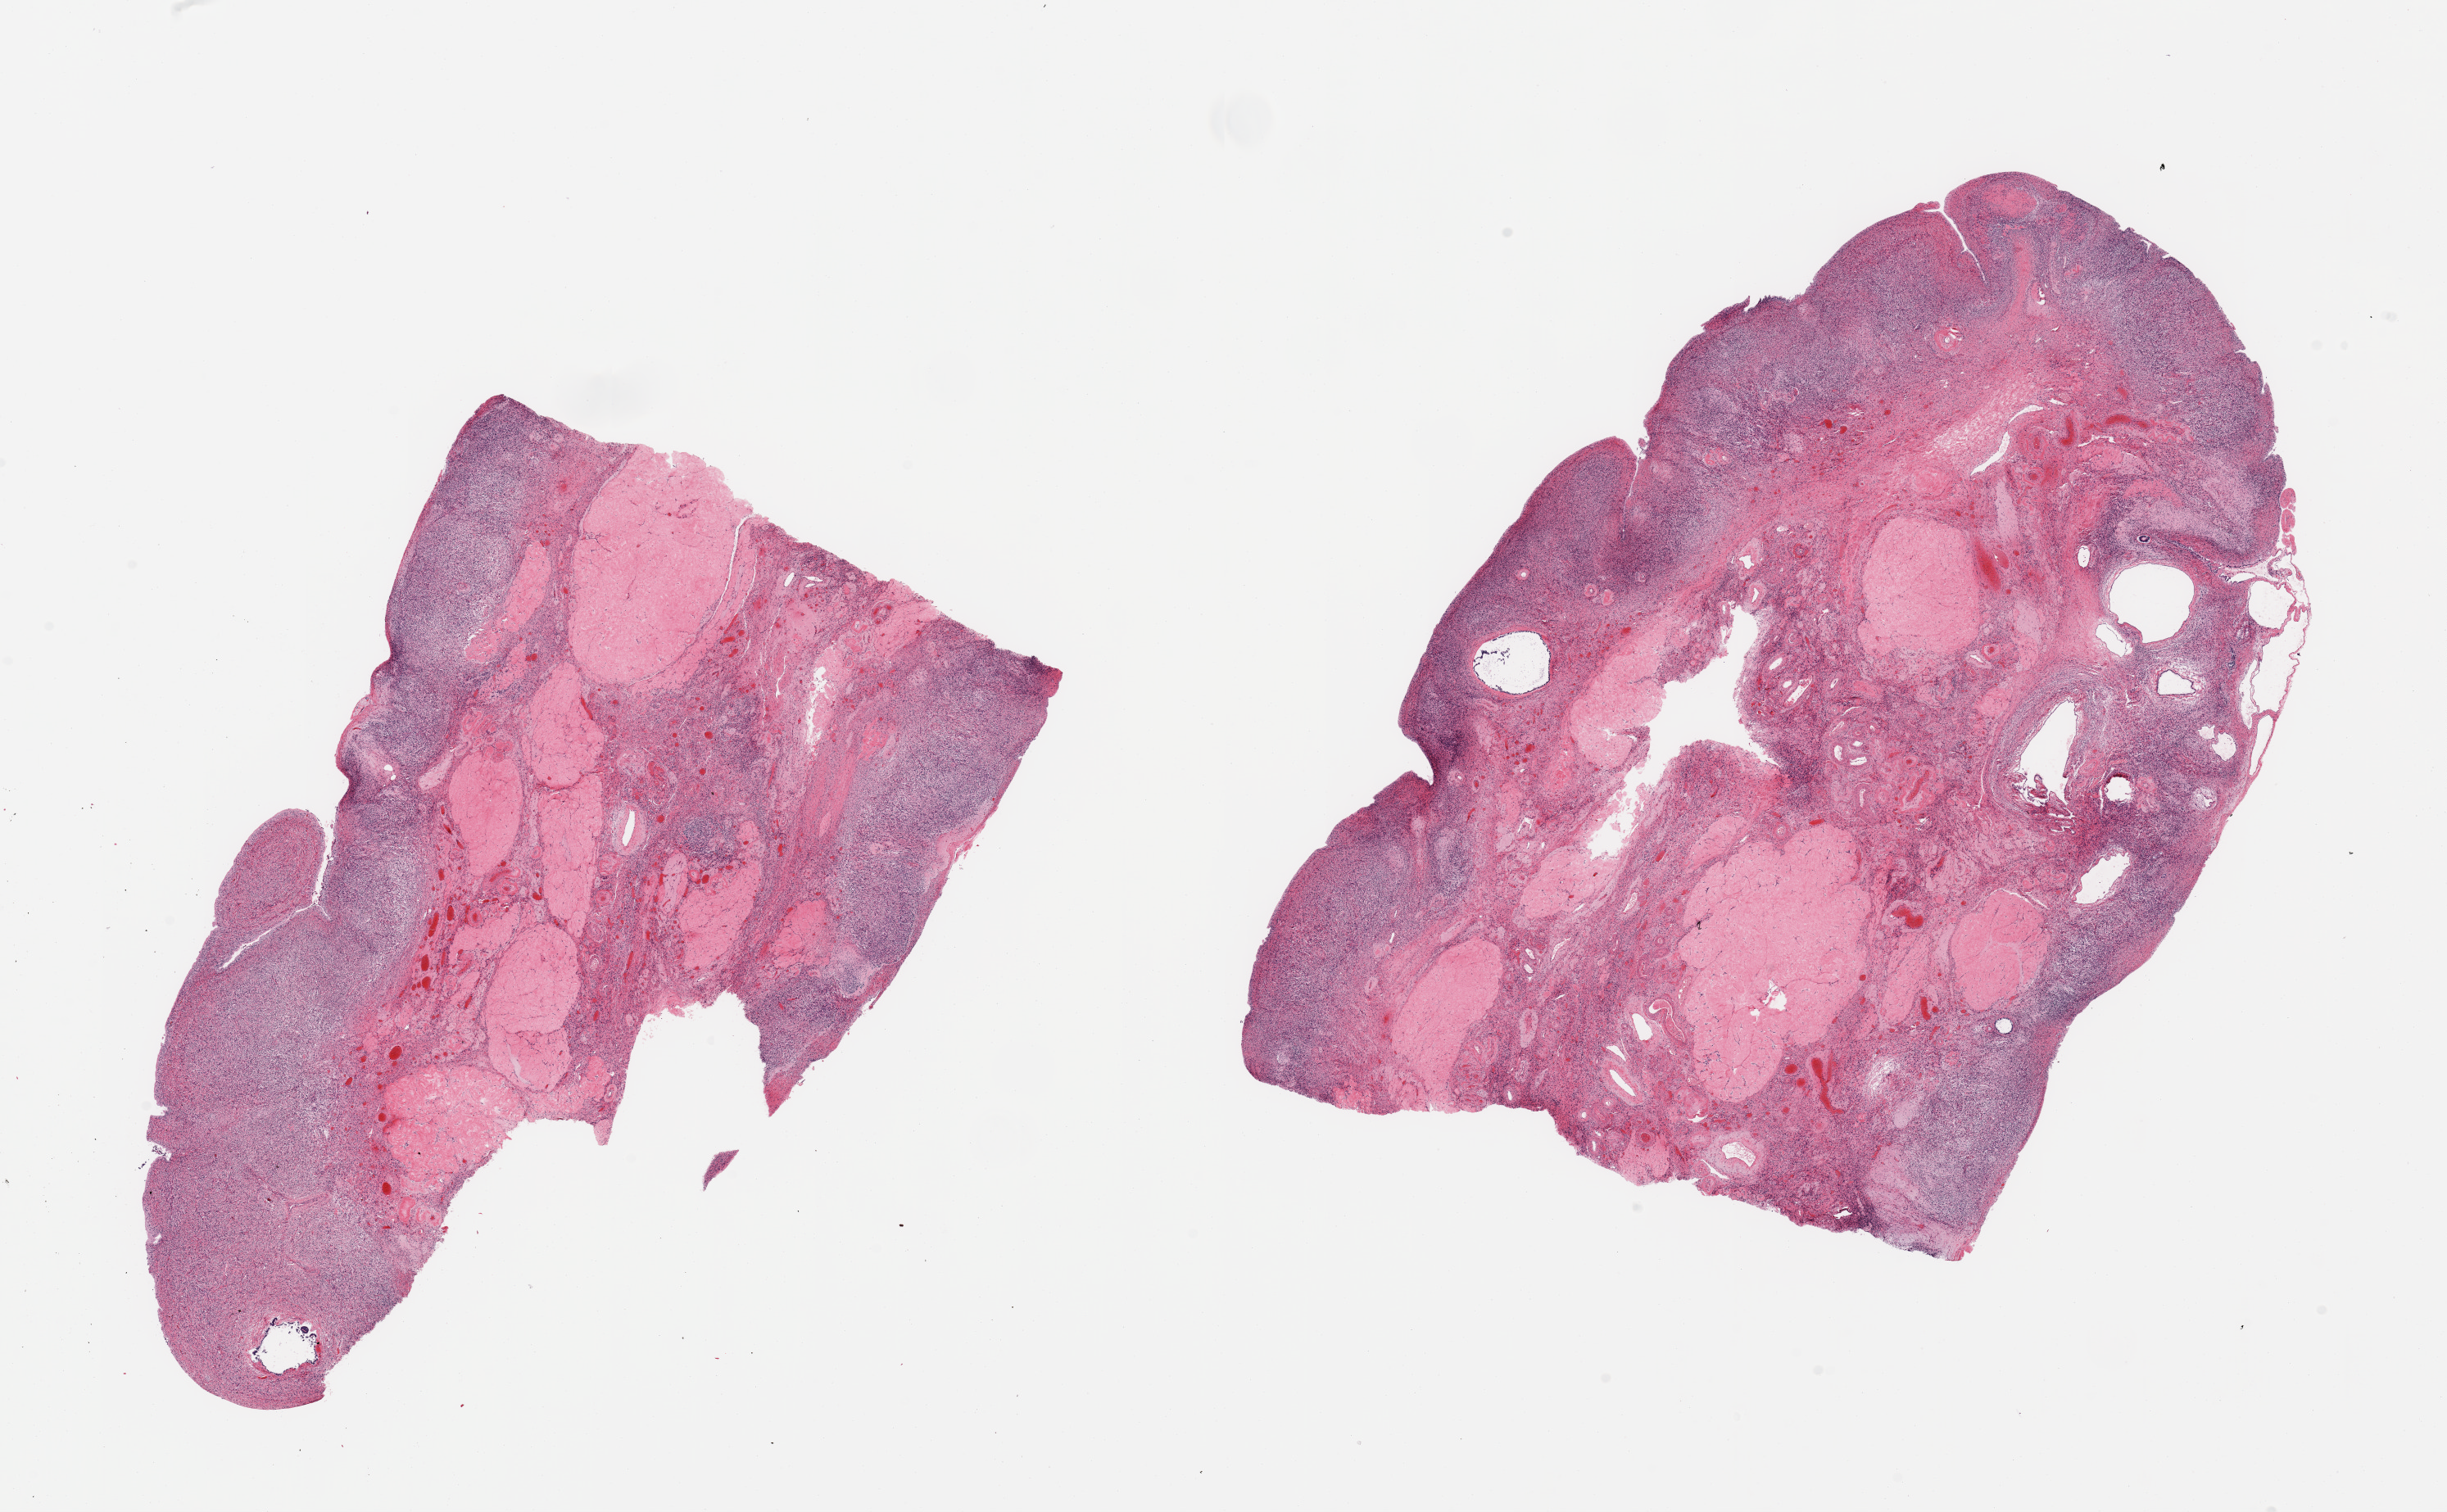
Hematoxylin and eosin (H&E) whole-slide image — whole scanned area (about 23.6 x 14.6 mm, slide scanned at 20x) shown as a low-resolution overview; PAXgene-fixed, paraffin-embedded tissue; section of ovary (target tissue); donor tissue sample. Female donor.
* review note (as recorded): 2 pieces, incidental simple serous cysts; Post menopausal atrophy